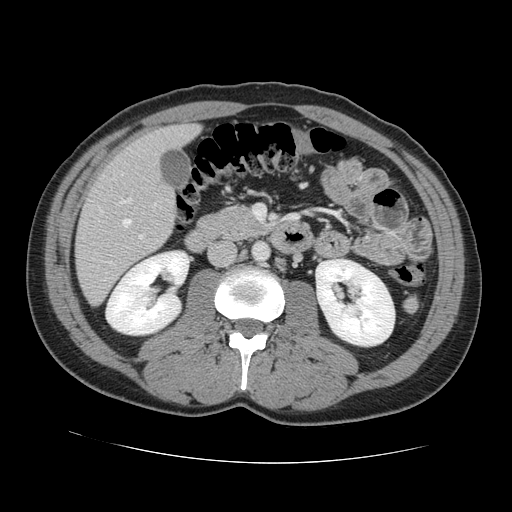
Contrast-enhanced abdominal CT, one axial slice. Position 49 of 131 along the scan axis. 120 kVp. Intravenous contrast given. Soft-tissue window (W 400 / L 40 HU). 2.5 mm slice thickness. 512 × 512 image matrix, field of view 380 × 380 mm. Male patient, age 40 years. Case-level facts recorded for this patient, not image findings: diagnosis: colorectal cancer liver metastases, imaged before liver resection; multiple liver metastases: yes; largest metastasis: 2.9 cm; disease in both lobes: yes.
Structures marked on this image (outlined manually by an expert reader):
- hepatic veins: bounding box (x1, y1, x2, y2) in pixels: (123, 219, 131, 227)
- liver: (76, 125, 198, 304)
- planned liver remnant (the part of the liver to remain after resection): (122, 125, 198, 168)
- portal vein (with intrahepatic branches): (120, 198, 144, 239)